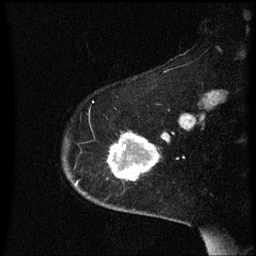
Breast MRI (dynamic contrast-enhanced), one sagittal slice. Slice 46 of 60 in the series (ordered by position). Dynamic contrast-enhanced series, image 2 of 3 at this slice position (ordered by acquisition). 1.5 T. TE 4.2 ms, TR 8.4 ms. 2 mm slice thickness. 256 × 256 image matrix, field of view 200 × 200 mm. Female patient, age 54 years. From the clinical record (not read from this slice): setting: breast cancer imaged before/during neoadjuvant chemotherapy; receptor status: HR-positive, HER2-negative.
Structures marked on this image (semi-automatically segmented with operator editing):
- analysis volume of interest (the breast-tissue region the enhancement analysis was run in; not a lesion): box from (x=108, y=134) to (x=170, y=185) px
- tumour enhancement mask (voxels above the 70 % enhancement threshold inside the analysis volume of interest): (x=108, y=134)–(x=170, y=181)